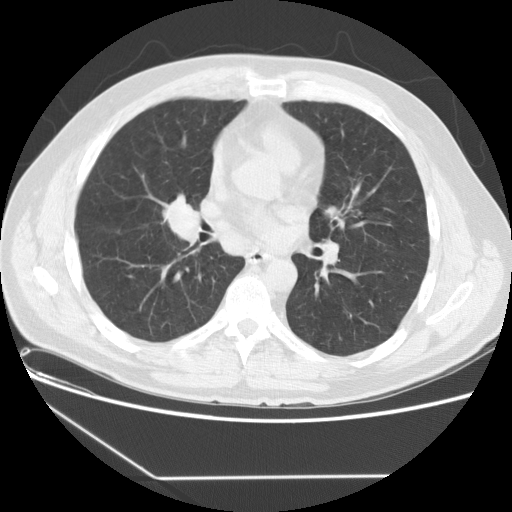
Low-dose screening chest CT, one axial slice; slice 77 of 154 in the series (ordered by position); lung window (W 1500 / L -600 HU); 2.5 mm slice thickness; 512 × 512 image matrix, field of view 370 × 370 mm.
Annotated regions visible in this slice (manually delineated by an expert):
- lesion 1 (tumor, middle lobe of right lung): bounding box <166,200,198,238> (left, top, right, bottom; pixels)